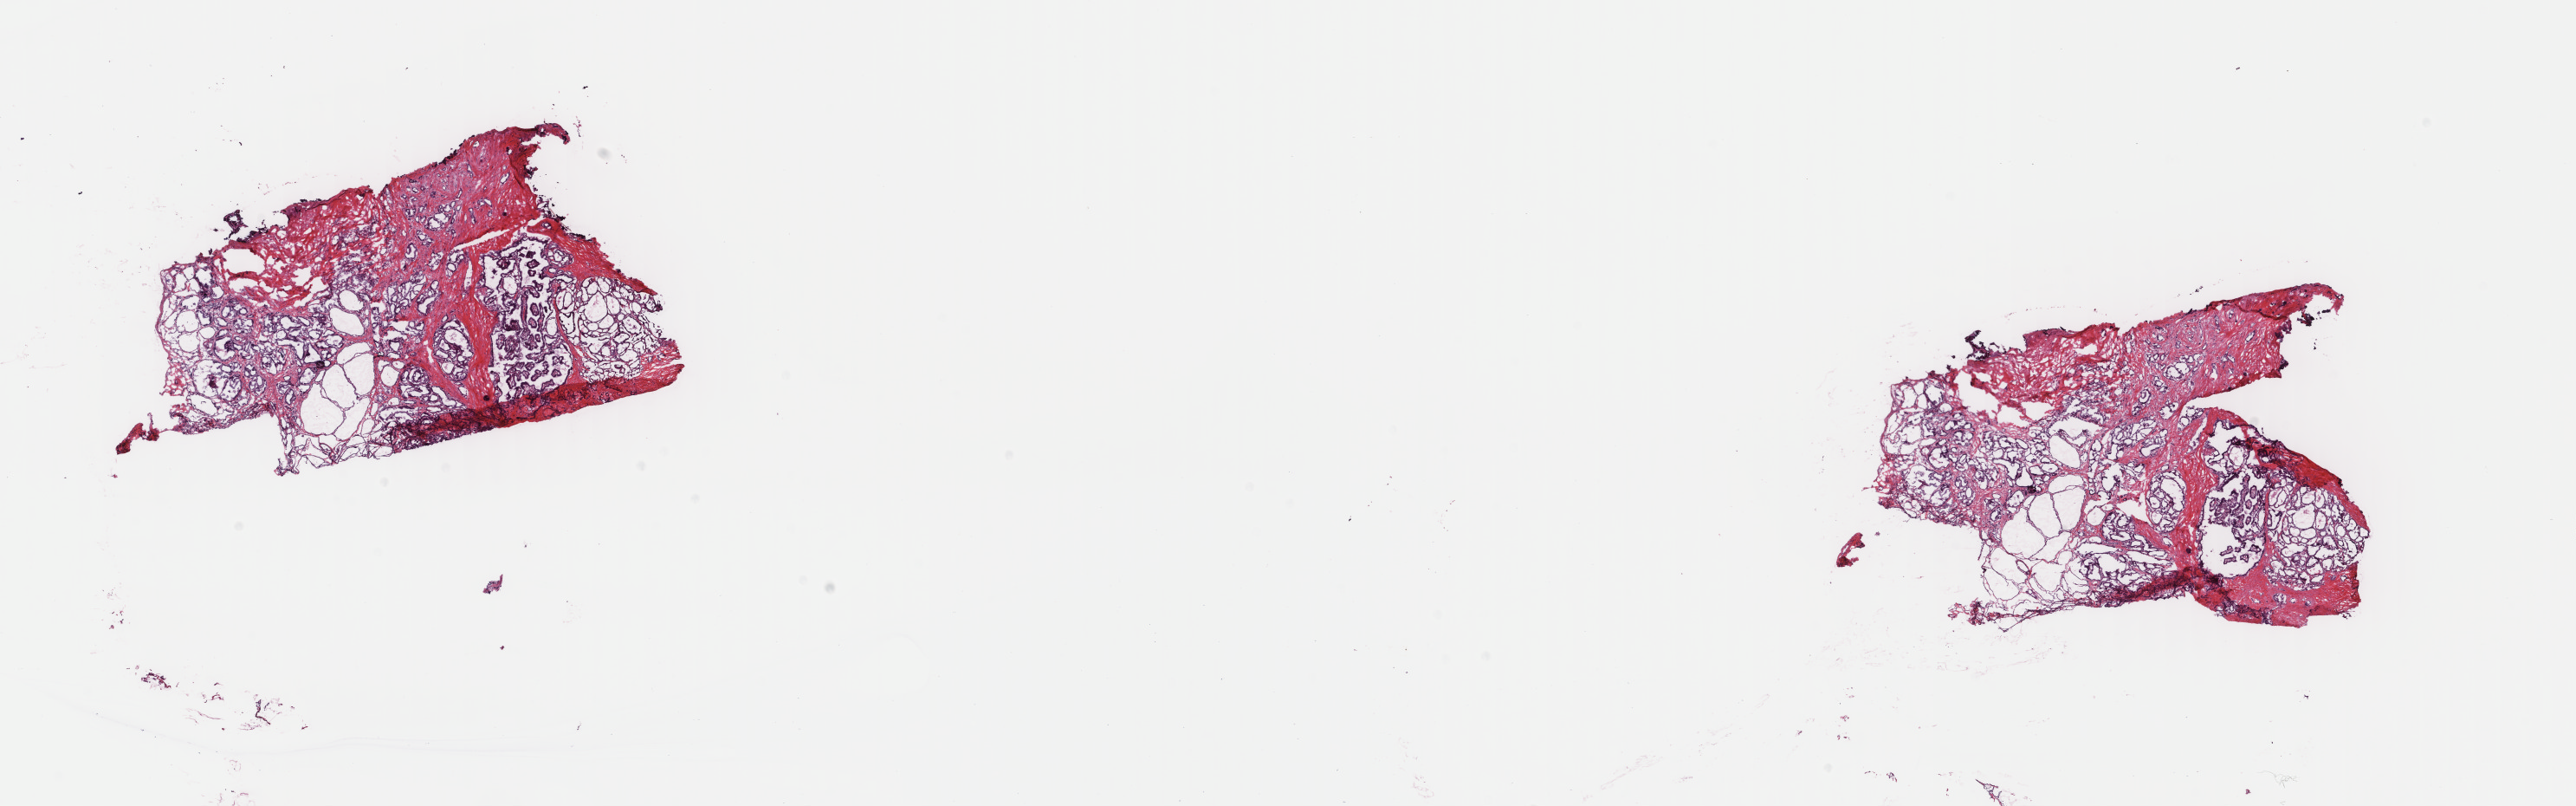
Whole-slide histology image, H&E — low-resolution overview of the scanned area, about 23.6 x 7.4 mm, frozen section from the top of the tissue portion, primary tumour sample from the thyroid. Male patient; age at initial diagnosis 41 years. Composition of this section per pathologist review: tumour cells 50%, tumour nuclei 95%, normal cells 0%, stromal cells 50%, necrosis 0%. Inflammatory infiltration, as recorded: lymphocyte infiltration 0%, monocyte infiltration 1%, neutrophil infiltration 0%.
* laterality: left
* pathologic diagnosis: Papillary adenocarcinoma, NOS (thyroid gland)
* AJCC pathologic stage: I (7th edition)
* lymph nodes positive (case pathology): 1 of 1 examined